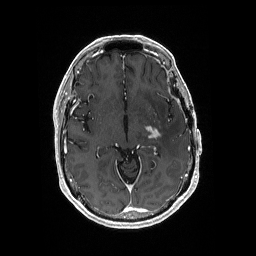
Brain MRI from a brain-tumour surgery series, one axial slice; position 106 of 176 along the scan axis; T1-weighted post-contrast; 1 mm slice thickness; 256 × 256 image matrix. Case-level facts recorded for this patient, not image findings: histopathology: Glioblastoma; WHO grade: 4; IDH mutation: no; tumour location: Left Medial Temporal.
Structures marked on this image (outlined manually by an expert reader):
- tumour: box from (x=144, y=123) to (x=163, y=139) px